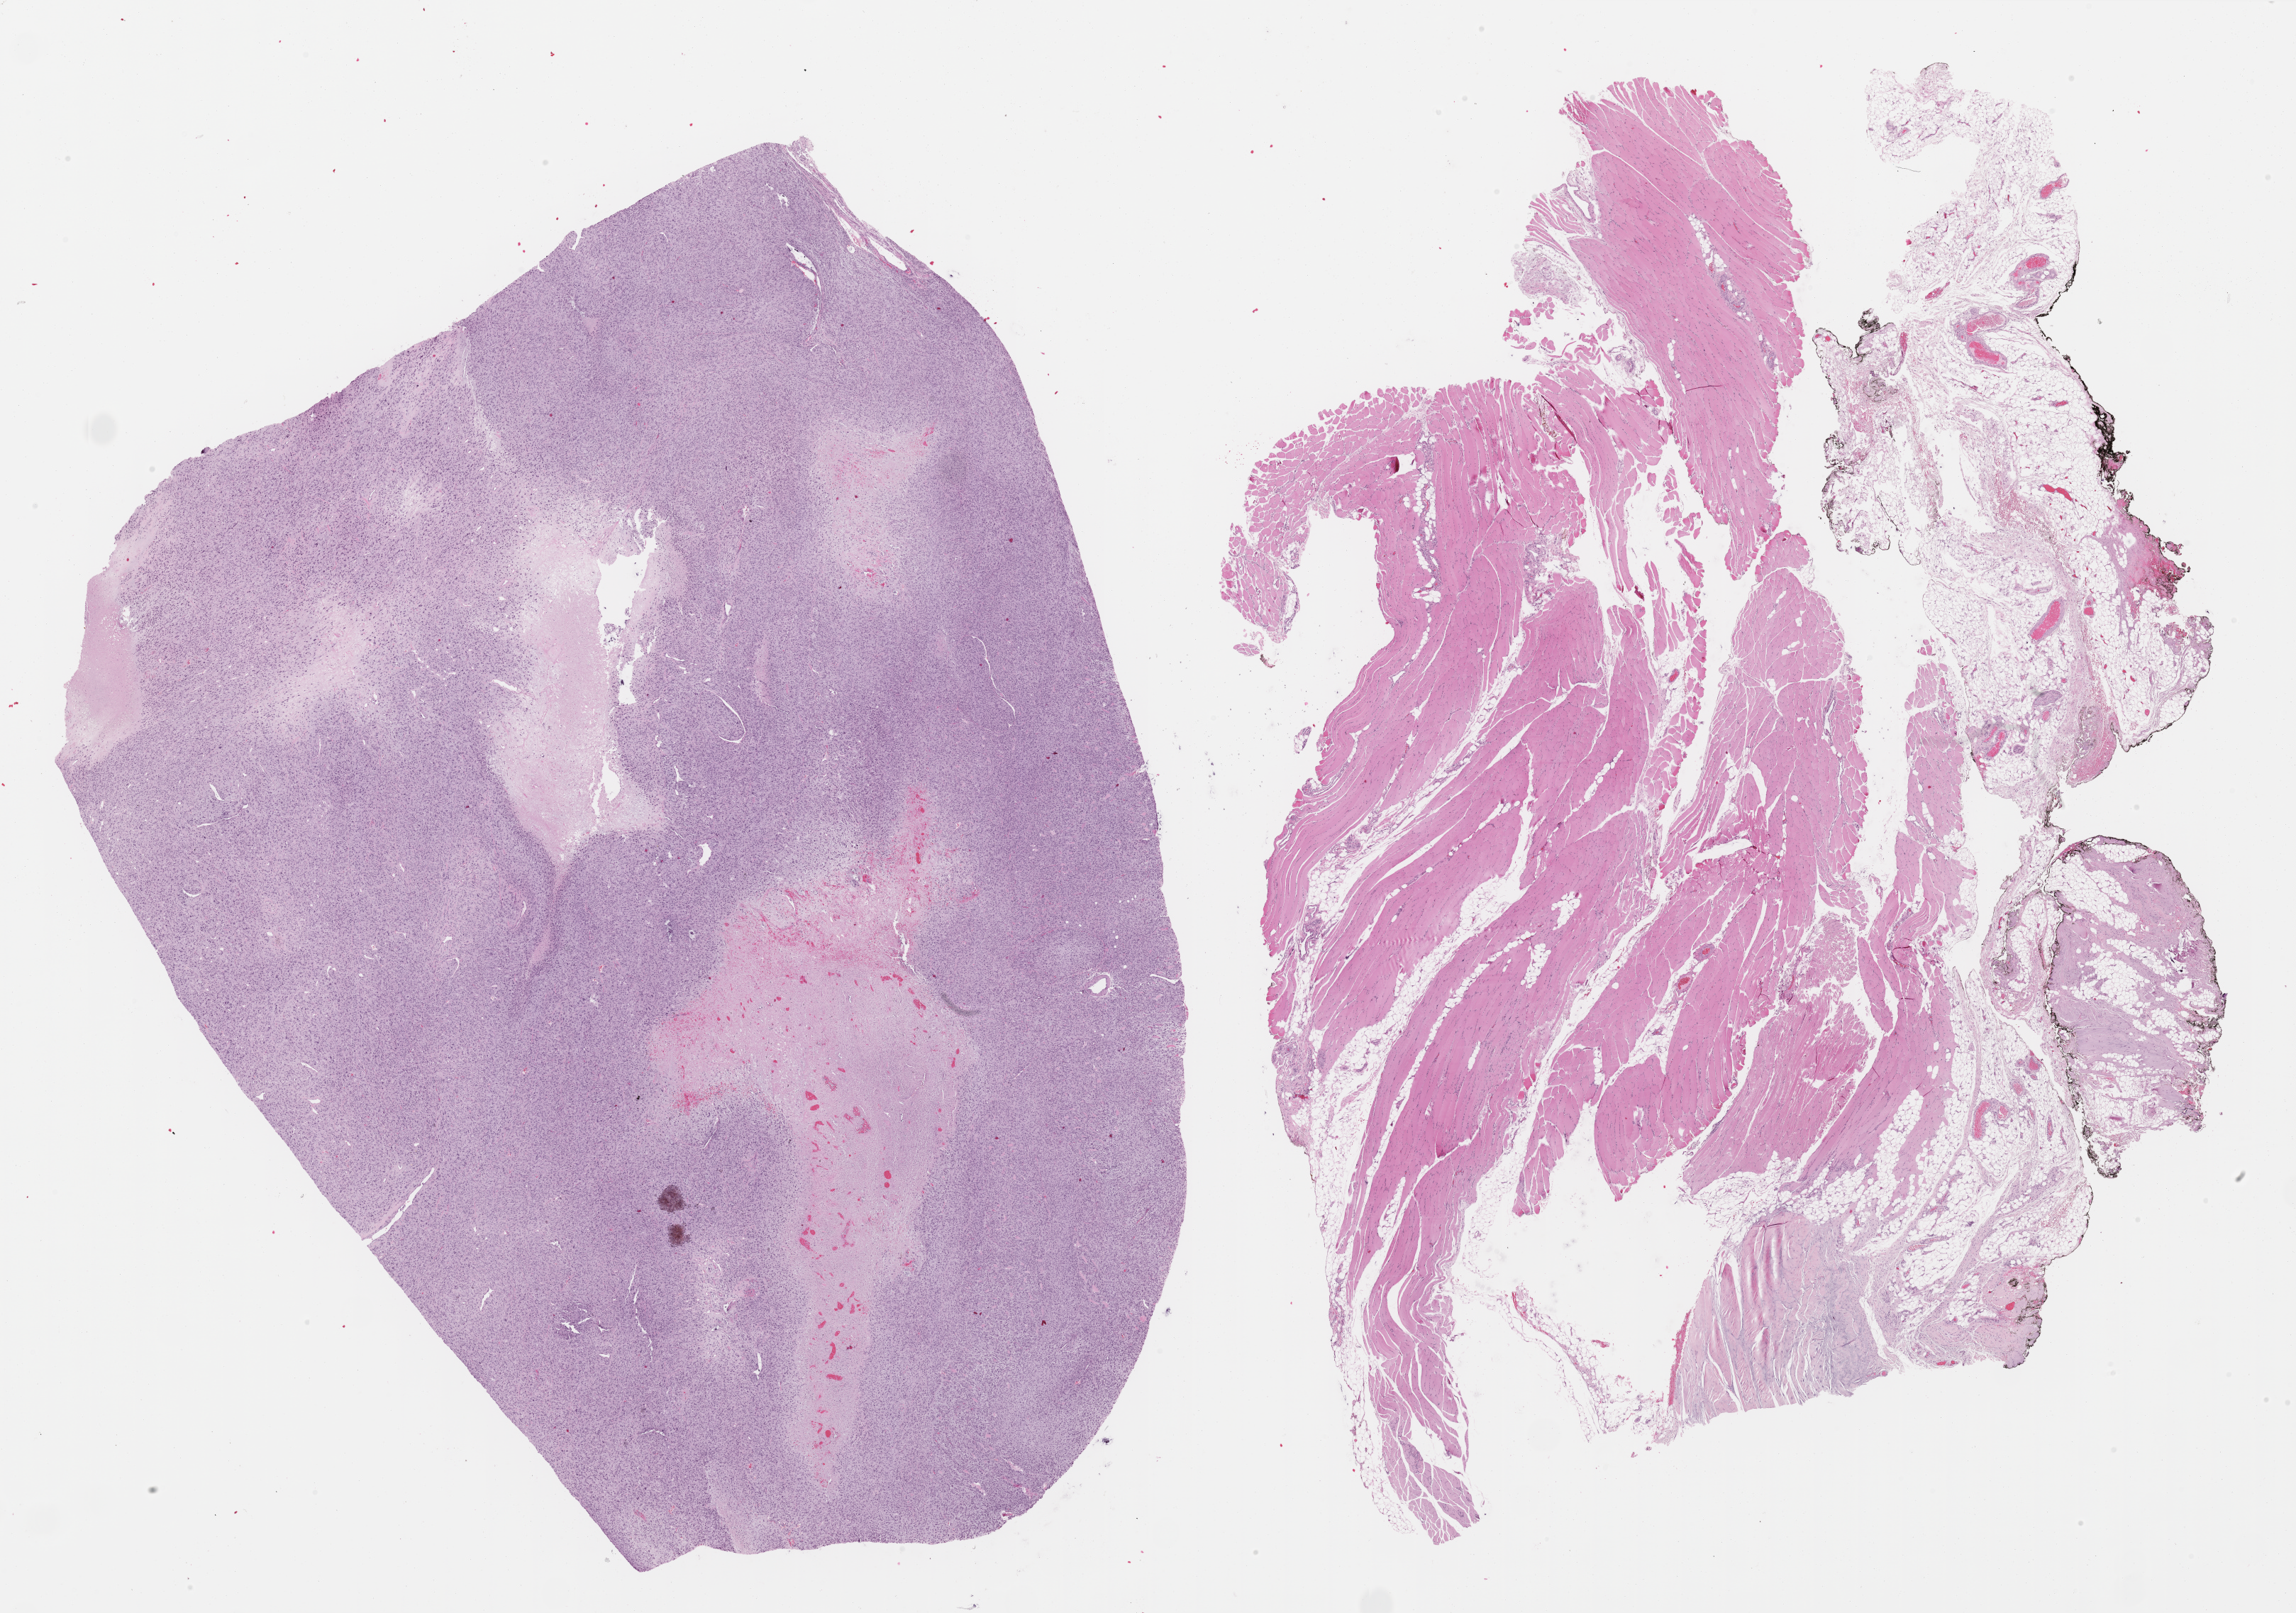
H&E whole-slide image — whole scanned area (about 26.2 x 18.4 mm) shown as a low-resolution overview, formalin-fixed paraffin-embedded (FFPE) diagnostic section, sample: primary tumour, connective, subcutaneous and other soft tissues. Patient: female, age at initial diagnosis 86 years.
Diagnosis: Fibromyxosarcoma (connective, subcutaneous and other soft tissues of pelvis).